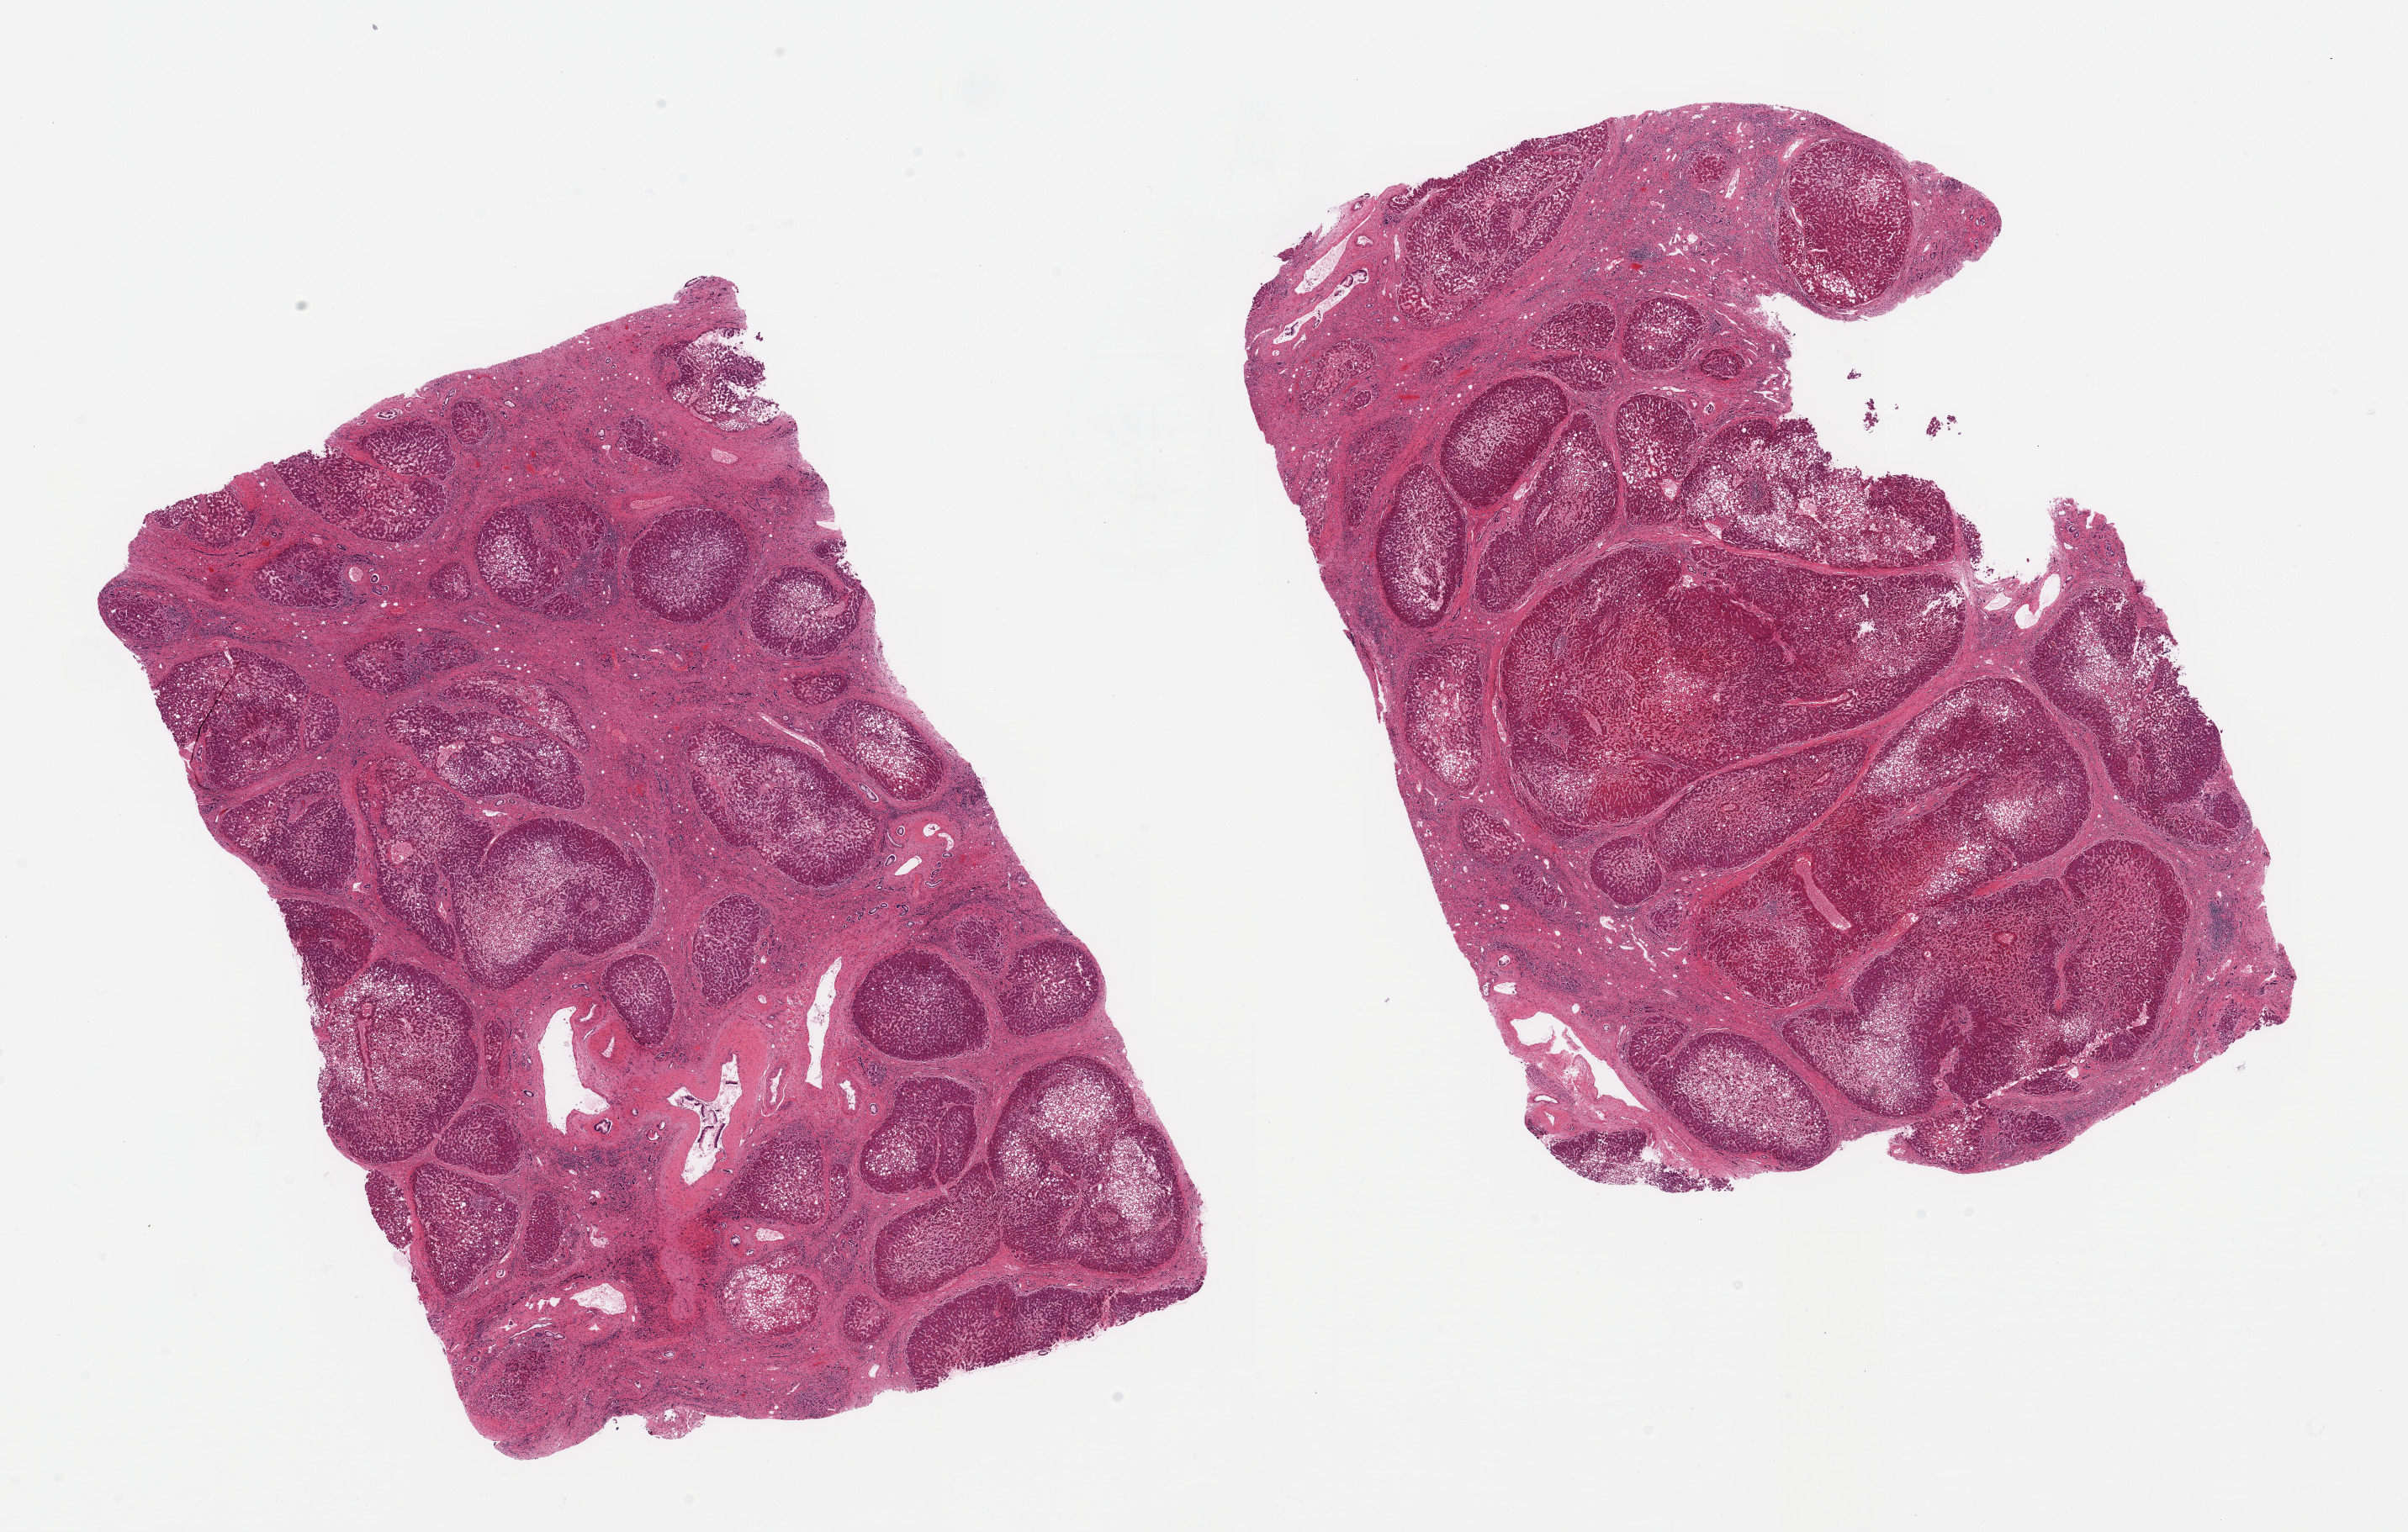
Digitized haematoxylin and eosin-stained section — whole scanned area (about 22.6 x 14.4 mm) shown as a low-resolution overview, PAXgene-fixed paraffin-embedded (PFPE) section, target tissue: liver, tissue donor sample. Donor sex: male.
Pathologist's review note for this sample: 2 pieces, advanced cirrhosis/steatosis, chronic hepatitis.